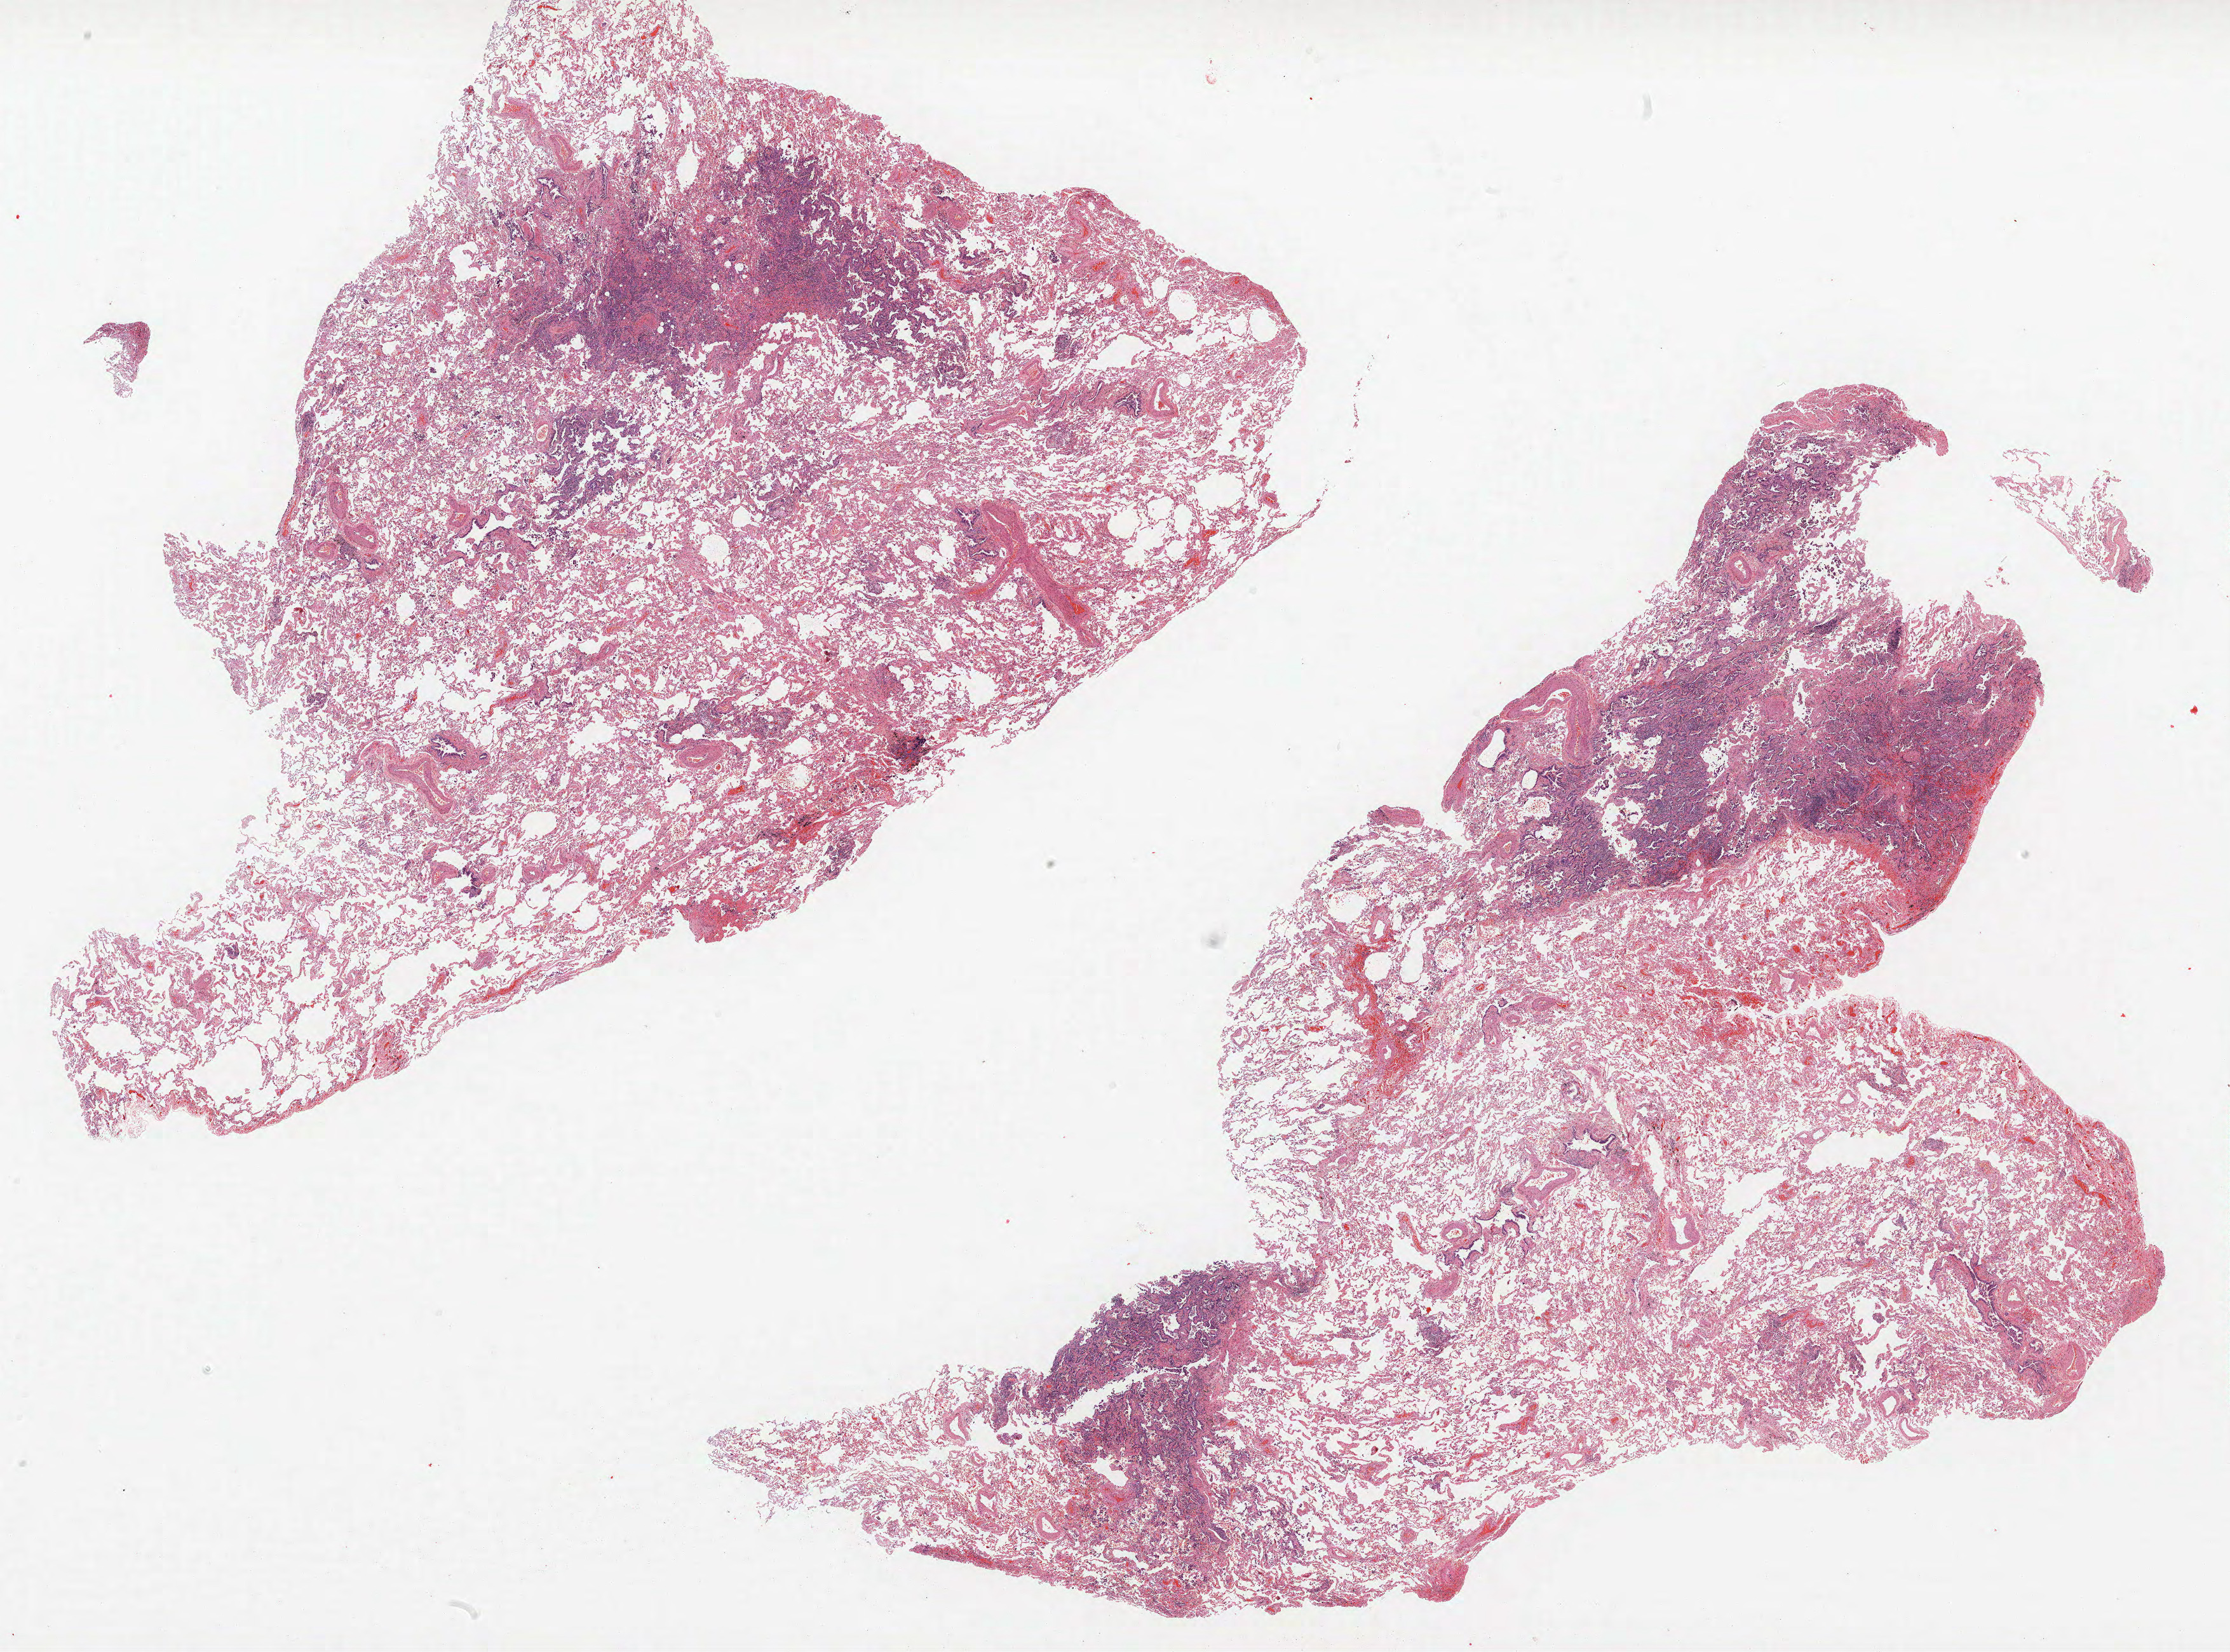
H&E whole-slide image — whole scanned area (about 28.1 x 20.8 mm, slide scanned at 40x) shown as a low-resolution overview. Formalin-fixed paraffin-embedded (FFPE) section. Lung. Female patient, aged 60 at enrolment. Former smoker at enrolment.
Participant's lung-cancer diagnosis: Acinar cell carcinoma.